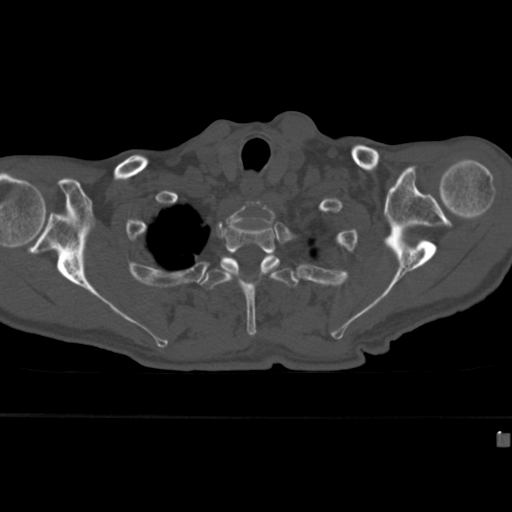
CT including the spine, one axial slice. Position 340 of 430 along the scan axis. Reconstruction kernel Br40s. 120 kVp. Bone window (W 1800 / L 400 HU). 1.5 mm slice thickness. 512 × 512 image matrix, field of view 337 × 337 mm. Male patient, age 64 years. Case-level facts recorded for this patient, not image findings: primary cancer: uterus.
Structures marked on this image (semi-automatically segmented with operator editing):
- T2 vertebra: bounding box [x1, y1, x2, y2] px = [222, 217, 280, 287]
- T3 vertebra: [200, 255, 299, 336]